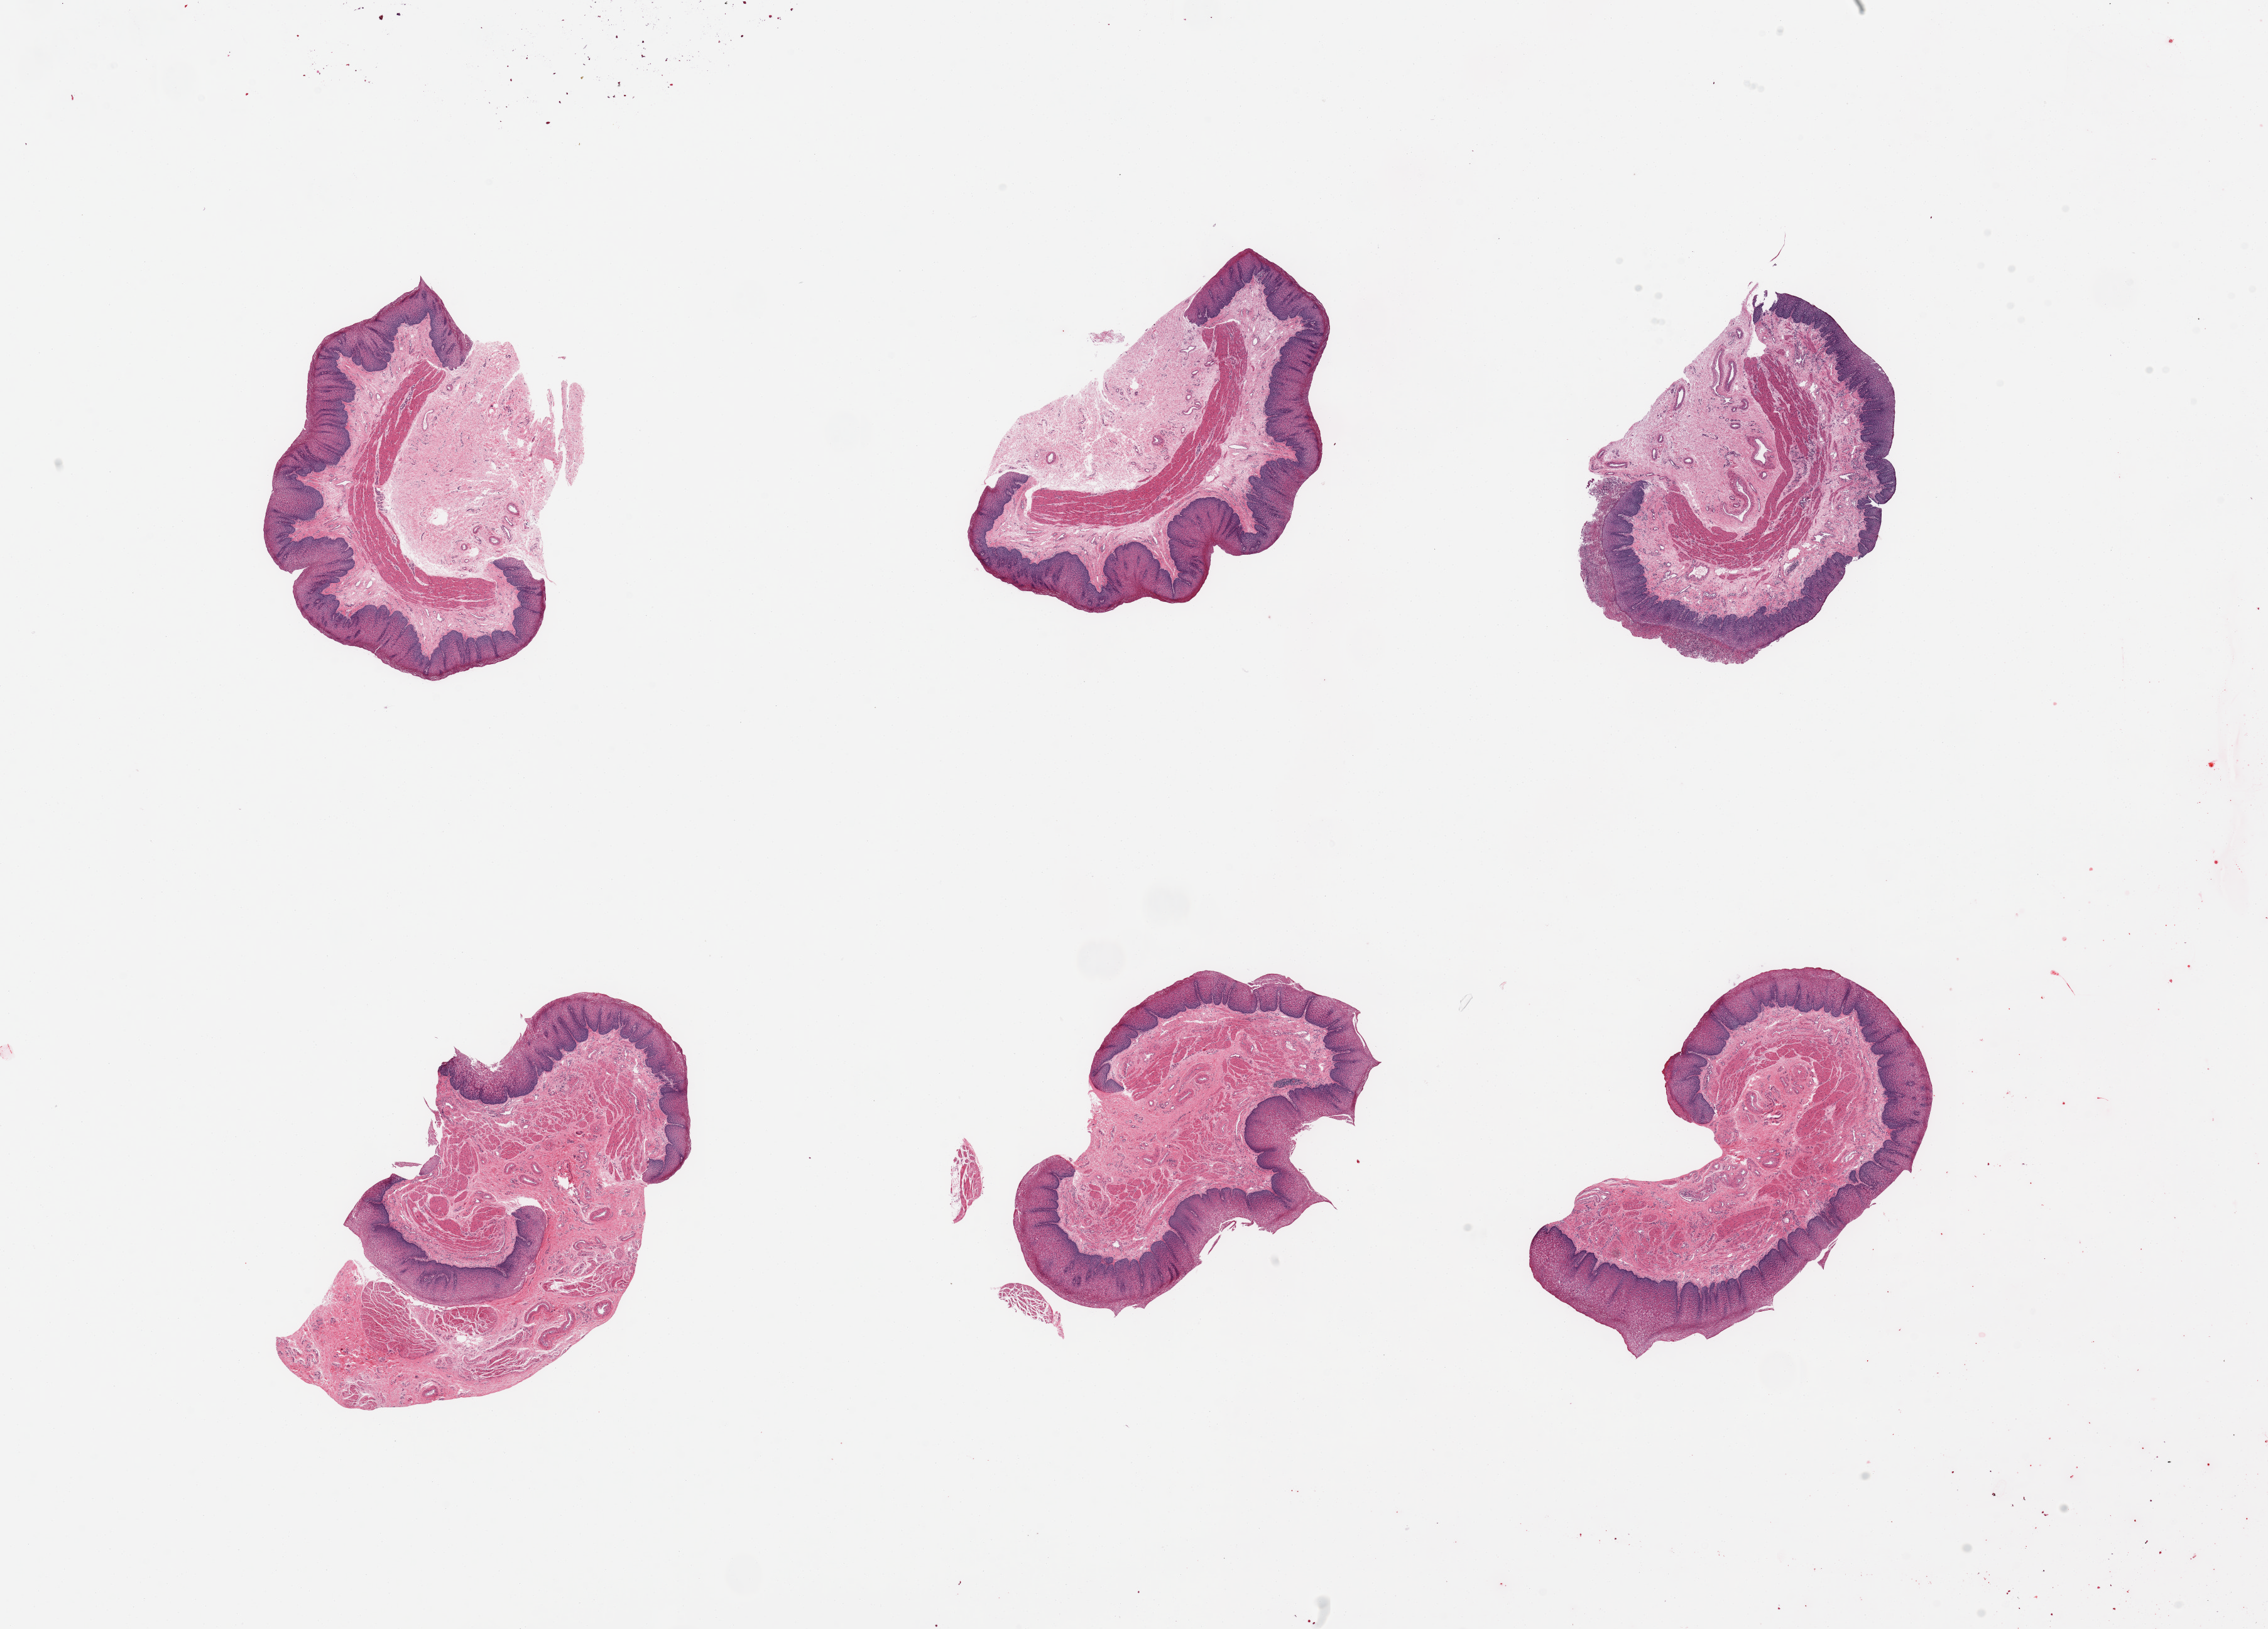
Digitized H&E-stained section, brightfield — low-resolution overview of the scanned area, about 28.5 x 20.5 mm (acquisition: 20x scan). PAXgene-fixed paraffin-embedded (PFPE) section. Sampled site (target tissue): esophageal mucous membrane. Donor tissue sample. Male donor.
* reviewer comment on this tissue sample: 6 pieces; parakeratosis with focal superficial exudate with possible fungal organisms; squamous hyperplasia (possible reflux)